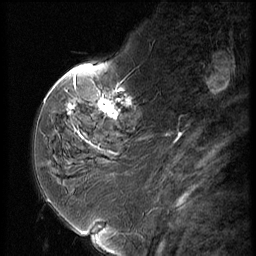
Breast MRI (dynamic contrast-enhanced), one sagittal slice; slice 17 of 56 in the series (ordered by position); dynamic contrast-enhanced series, image 2 of 3 at this slice position (ordered by acquisition); 1.5 T; TE 4.2 ms, TR 9 ms; 256 × 256 image matrix, field of view 180 × 180 mm. Patient: female, 59 years. From the clinical record (not read from this slice): setting: breast cancer imaged before/during neoadjuvant chemotherapy; receptor status: HER2-positive.
Structures marked on this image (semi-automatically segmented with operator editing):
- analysis volume of interest (the breast-tissue region the enhancement analysis was run in; not a lesion): box from (x=44, y=66) to (x=151, y=135) px
- tumour enhancement mask (voxels above the 140 % enhancement threshold inside the analysis volume of interest): (x=68, y=98)–(x=127, y=118)